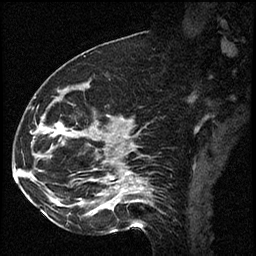
Breast MRI (dynamic contrast-enhanced), one sagittal slice; position 28 of 60 along the scan axis; dynamic contrast-enhanced series, image 2 of 2 at this slice position (ordered by acquisition); 1.5 T; TE 4.2 ms, TR 17.3 ms; 256 × 256 image matrix, field of view 200 × 200 mm. Female patient. From the clinical record (not read from this slice): setting: breast cancer imaged before/during neoadjuvant chemotherapy; receptor status: HR-positive, HER2-negative.
Structures marked on this image (semi-automatically segmented with operator editing):
- analysis volume of interest (the breast-tissue region the enhancement analysis was run in; not a lesion): bounding box <41,93,115,223> (left, top, right, bottom; pixels)
- tumour enhancement mask (voxels above the 100 % enhancement threshold inside the analysis volume of interest): <58,127,63,133>